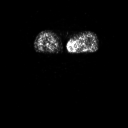
FDG PET of an extremity soft-tissue mass (from a PET/CT study), one axial slice. Slice 3 of 91 in the series (ordered by position). 128 × 128 image matrix, field of view 700 × 700 mm. Female patient, age 74 years. From the clinical record (not read from this slice): histological type: pleomorphic leiomyosarcoma; grade: high; site of the primary tumour: left thigh.
Annotated regions visible in this slice (expert contour drawn on MRI and transferred to this co-registered scan by the dataset authors):
- gross tumour volume including surrounding oedema: bounding box [x1, y1, x2, y2] px = [73, 36, 87, 51]